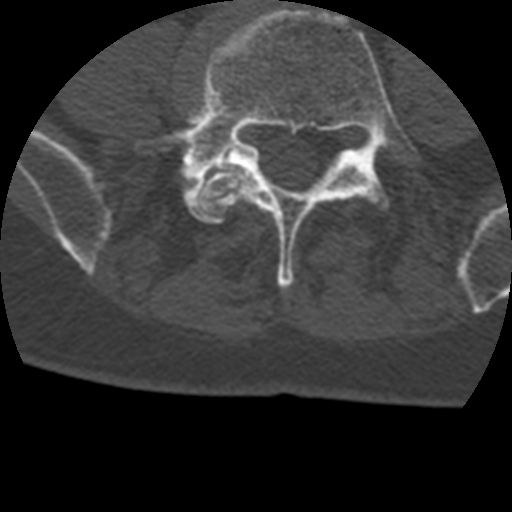
CT including the spine, one axial slice. Position 47 of 399 along the scan axis. Reconstruction kernel STANDARD. Bone window (W 1800 / L 400 HU). 1.25 mm slice thickness. 512 × 512 image matrix, field of view 160 × 160 mm. Patient age 69 years. From the clinical record (not read from this slice): primary cancer: prostate.
Annotated regions visible in this slice (semi-automatic segmentation, software-assisted and operator-edited):
- L4 vertebra: bounding box <197,170,247,221> (left, top, right, bottom; pixels)
- L5 vertebra: <135,9,422,290>